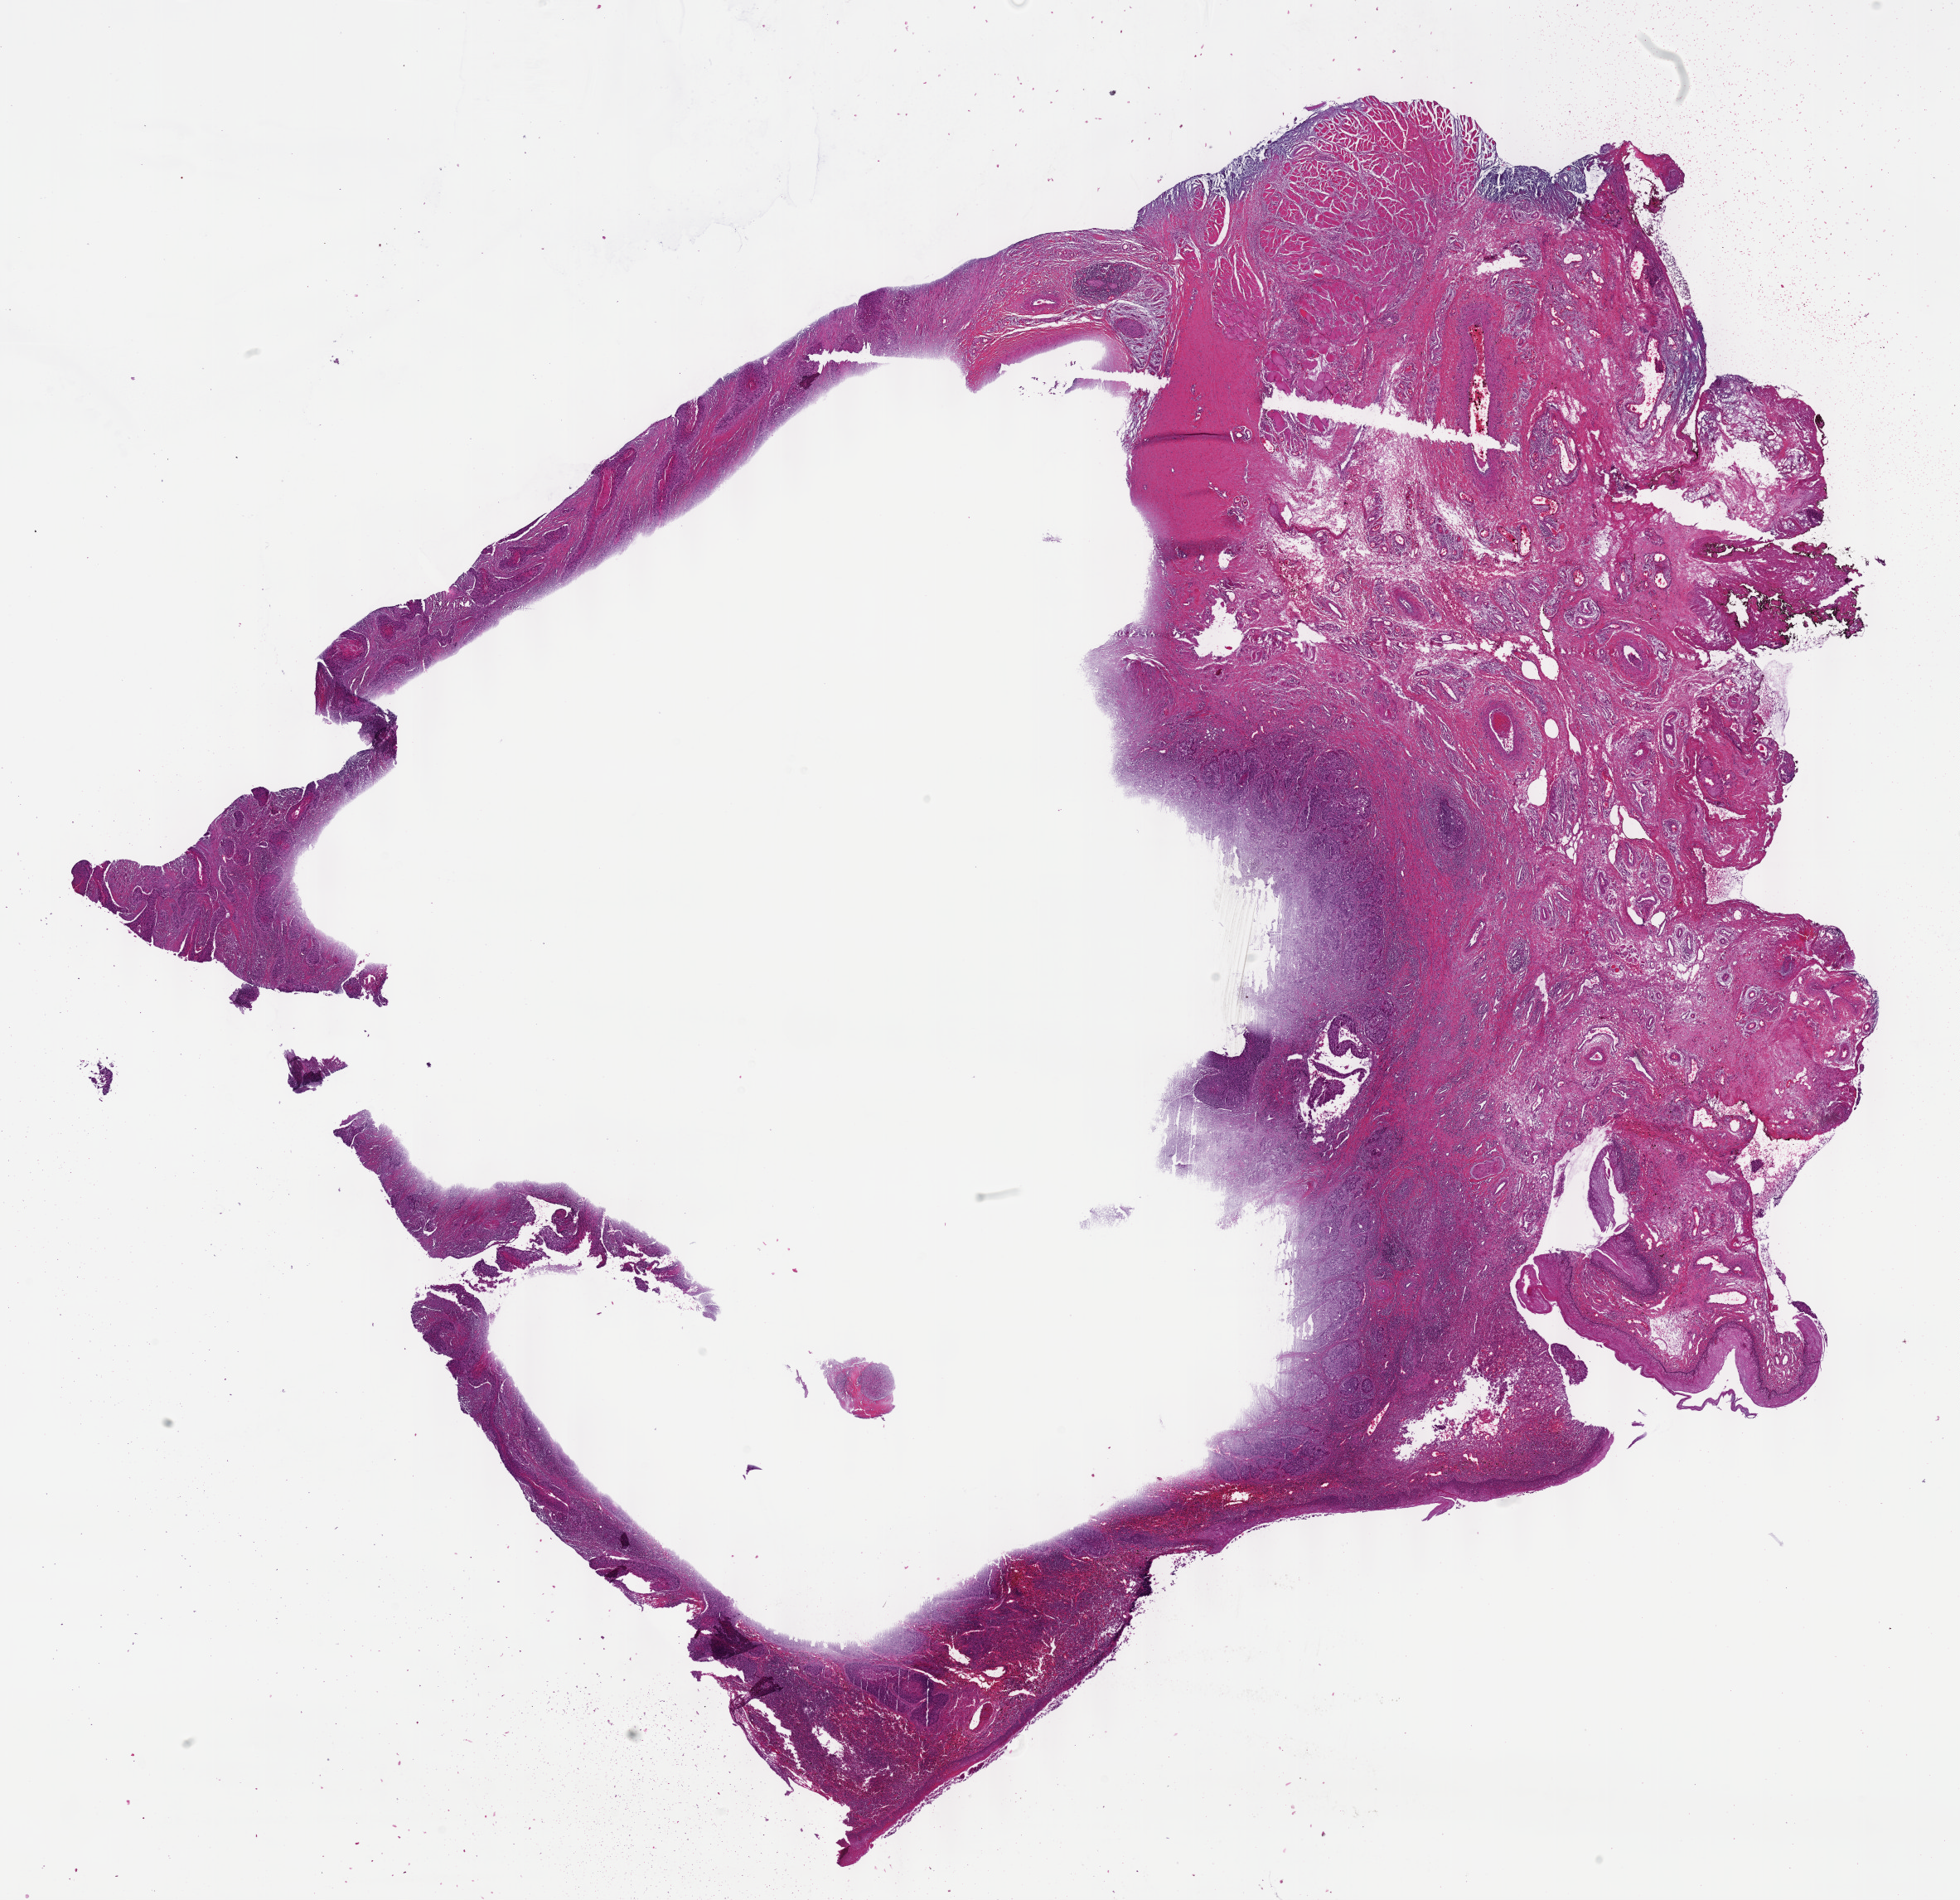
Digitized H&E-stained tissue section (whole slide) — shown as a low-resolution overview of the whole scanned area (about 19.1 x 18.5 mm, acquisition: 40x scan). Formalin-fixed paraffin-embedded (FFPE) diagnostic section. Primary tumour sample from the head and neck. Patient: male, age at initial diagnosis 61 years. Histologic grade: GX (grade cannot be assessed).
* diagnosis: Squamous cell carcinoma, NOS (larynx, NOS)
* TNM: T2 N1
* AJCC pathologic stage: III (7th edition)